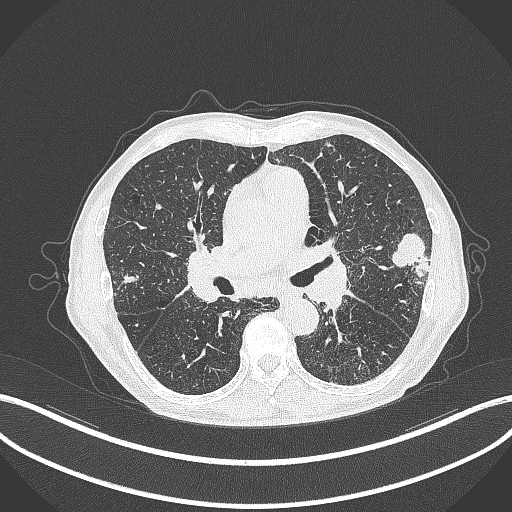
Chest CT, one axial slice; slice 228 of 463 in the series (ordered by position); lung window (W 1500 / L -600 HU); 512 × 512 image matrix, field of view 400 × 400 mm. Patient: male, 74 years. From the clinical record (not read from this slice): clinical TNM (as recorded): T2a N1 M0.
Outlined on this slice (bounding box drawn by a radiologist):
- lung tumour (recorded histology: adenocarcinoma): bounding box [x1, y1, x2, y2] px = [391, 232, 432, 276]